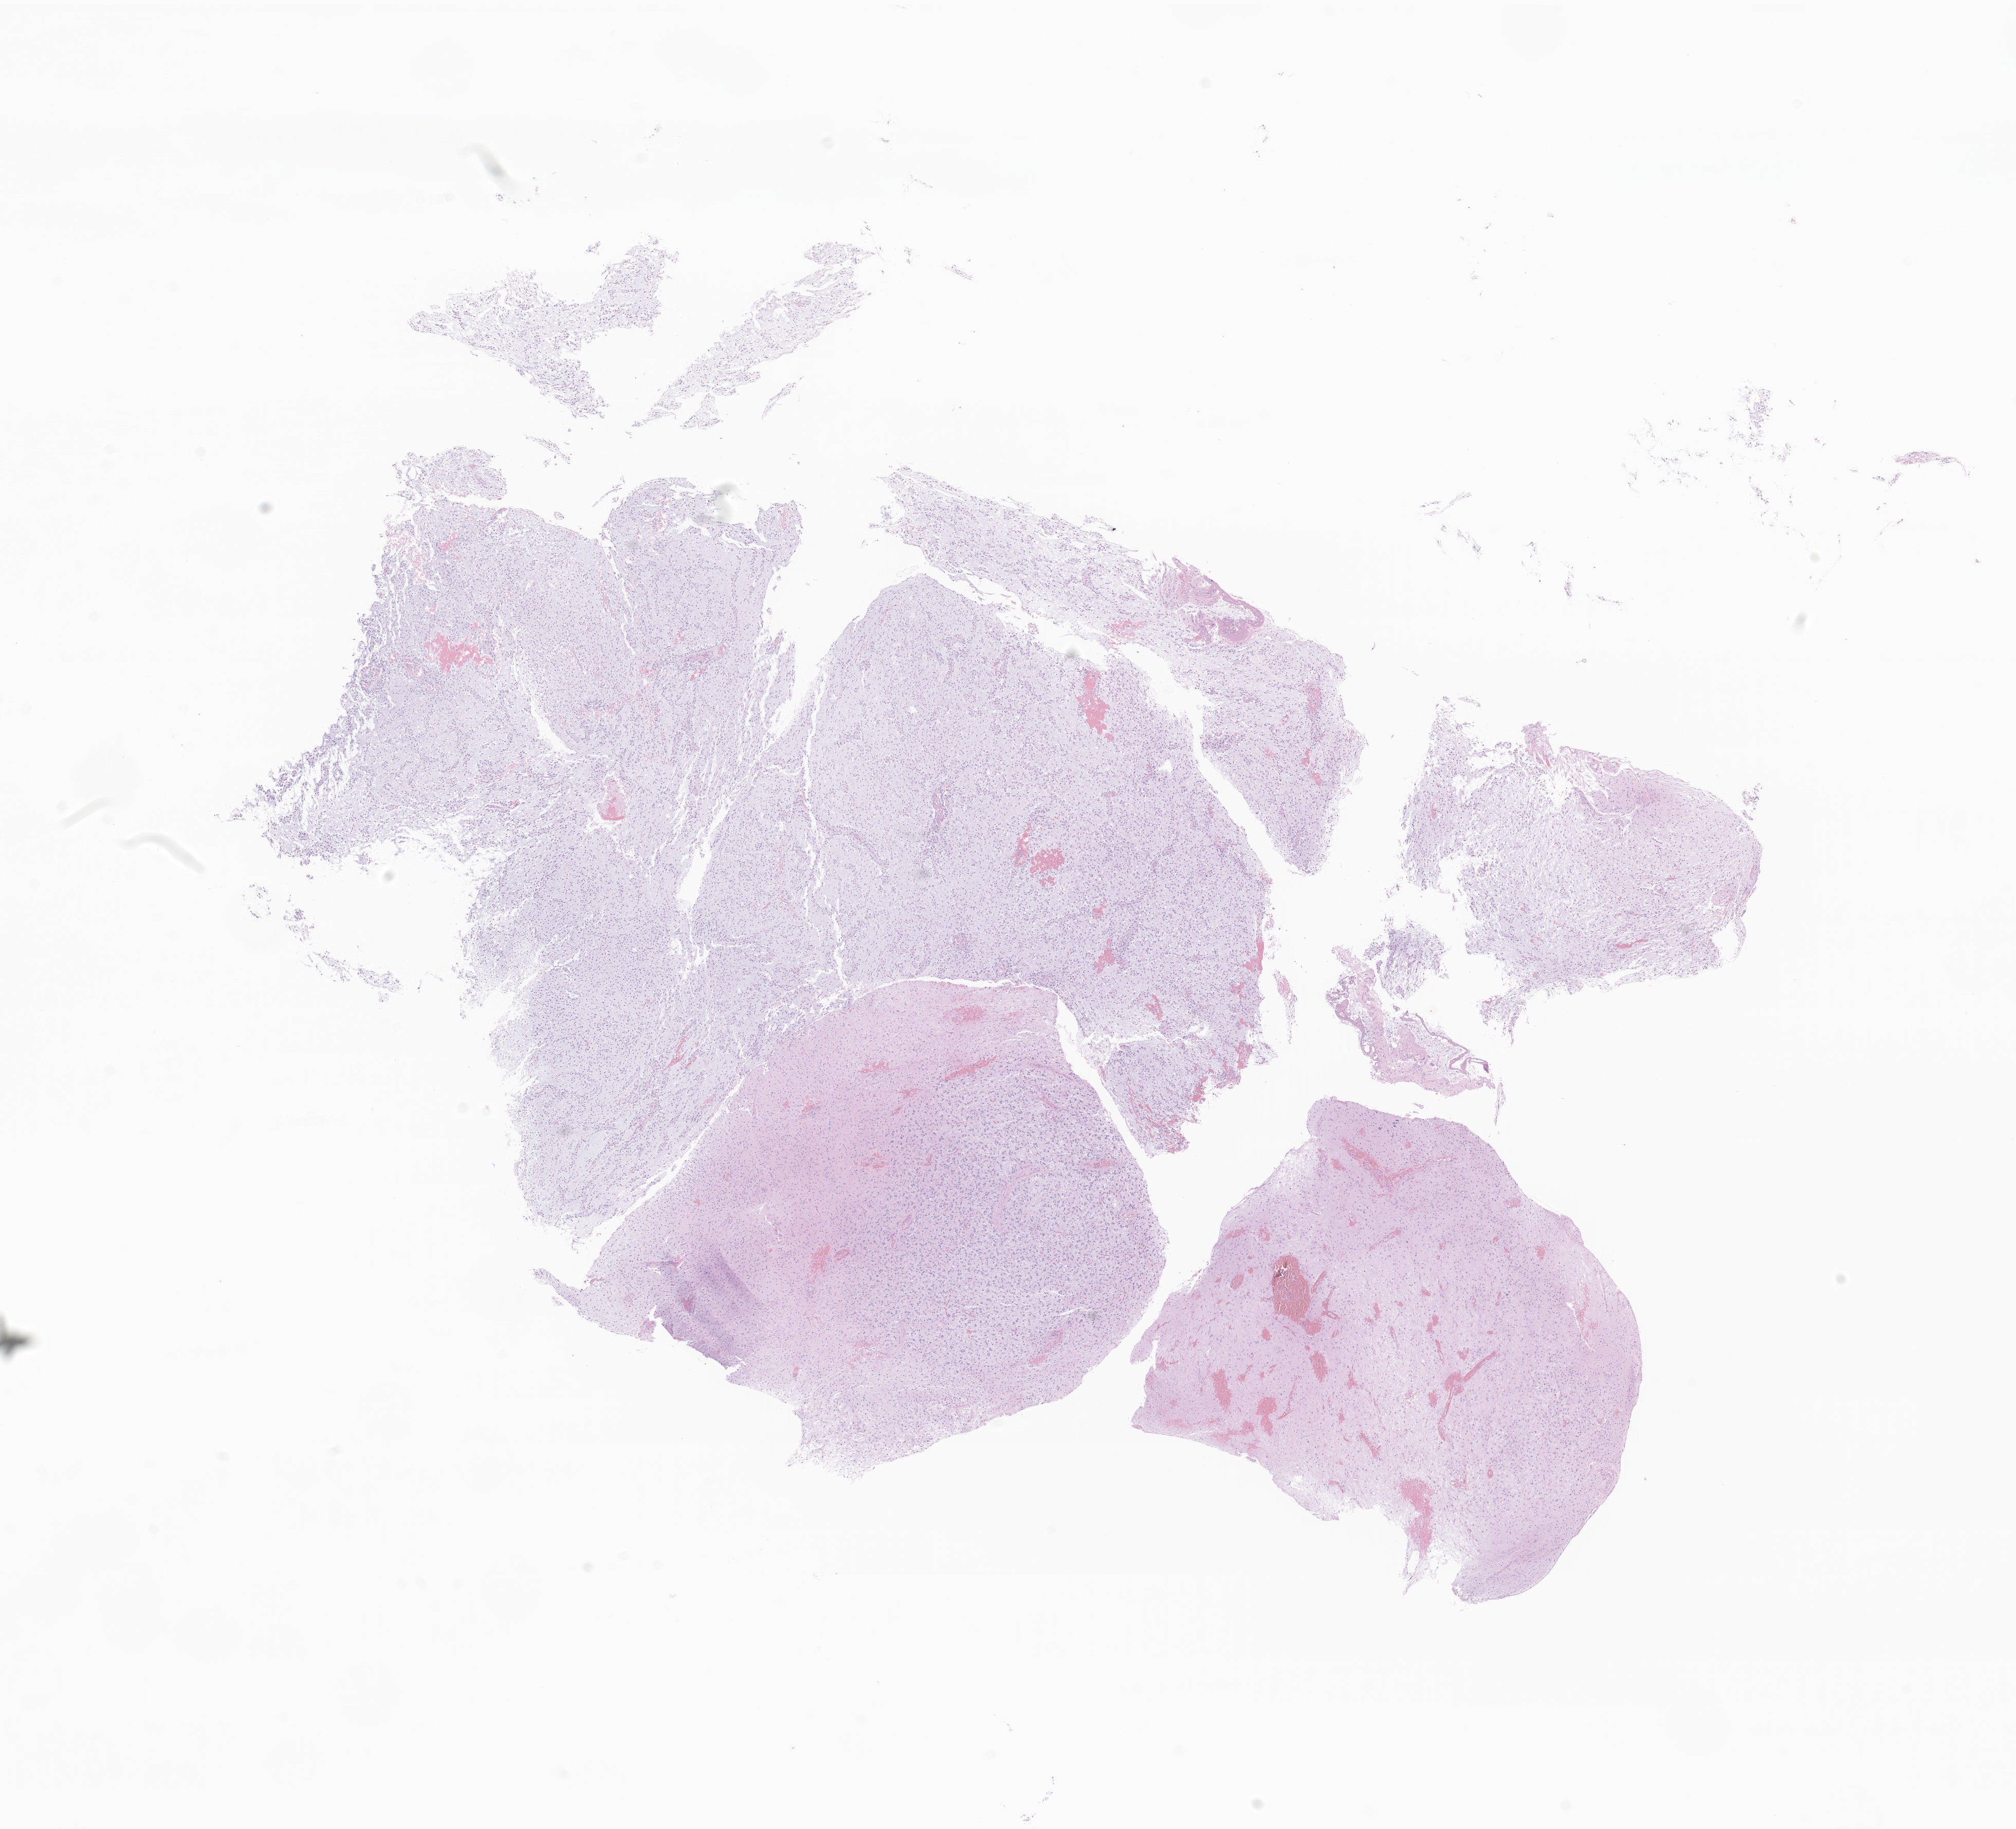
Whole-slide image, H&E stain of tumor tissue from the temporal lobe — low-resolution overview of the scanned area, about 16.5 x 15.0 mm; formalin-fixed paraffin-embedded section. Patient: male, age 110 months (9 years 2 months).
Diagnosis (ICD-O-3 morphology term): Pilocytic astrocytoma.